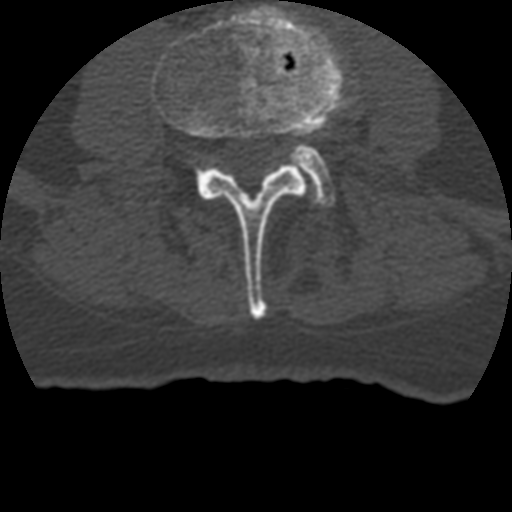
CT including the spine, one axial slice; slice 83 of 399 in the series (ordered by position); 120 kVp; bone window (W 1800 / L 400 HU); 1.25 mm slice thickness; 512 × 512 image matrix, field of view 160 × 160 mm. Patient age 69 years. Case-level facts recorded for this patient, not image findings: primary cancer: prostate.
Annotated regions visible in this slice (semi-automatic segmentation, software-assisted and operator-edited):
- L3 vertebra: bounding box [x1, y1, x2, y2] px = [152, 5, 347, 319]
- L4 vertebra: [291, 144, 336, 211]